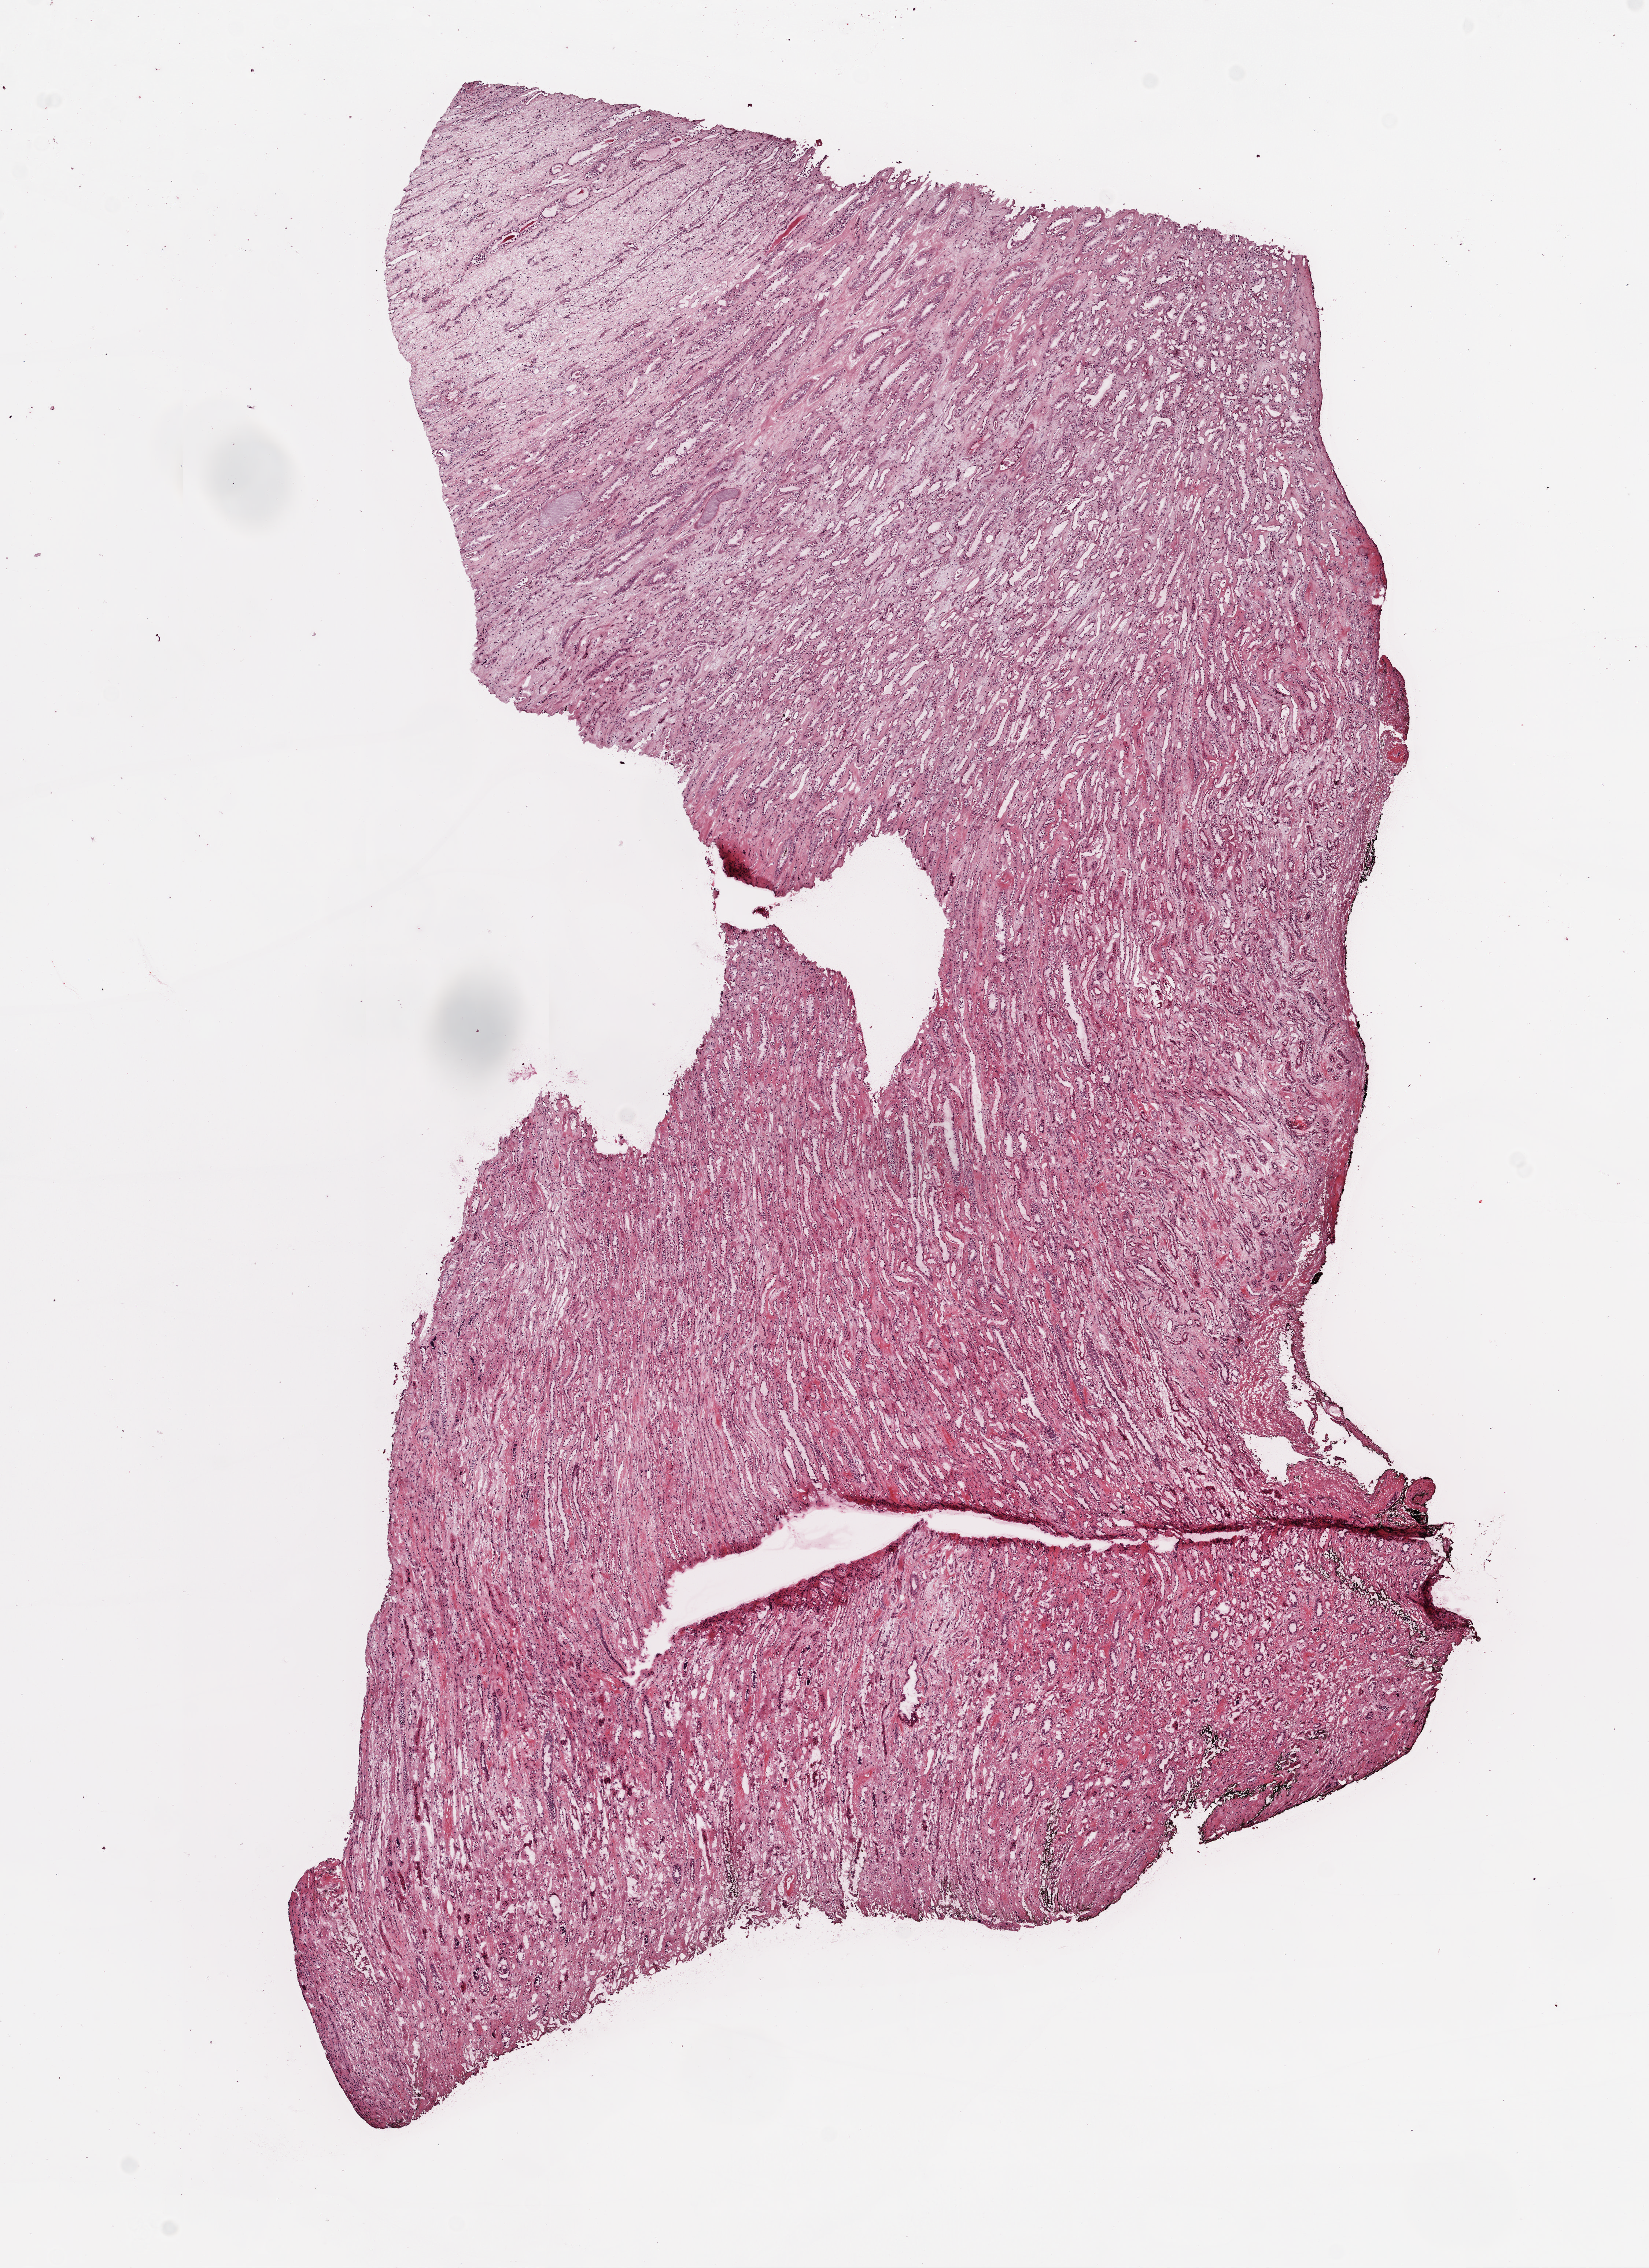
H&E whole-slide image, a low-resolution overview of the entire scanned area, about 9.0 x 12.4 mm (acquisition: 20x scan); frozen section from the top of the tissue portion; kidney, solid tissue normal (non-tumour tissue) sample. Female, age 72 years at initial diagnosis.
This section: solid tissue normal sample (biorepository sample class). Patient diagnosis: Clear cell adenocarcinoma, NOS.